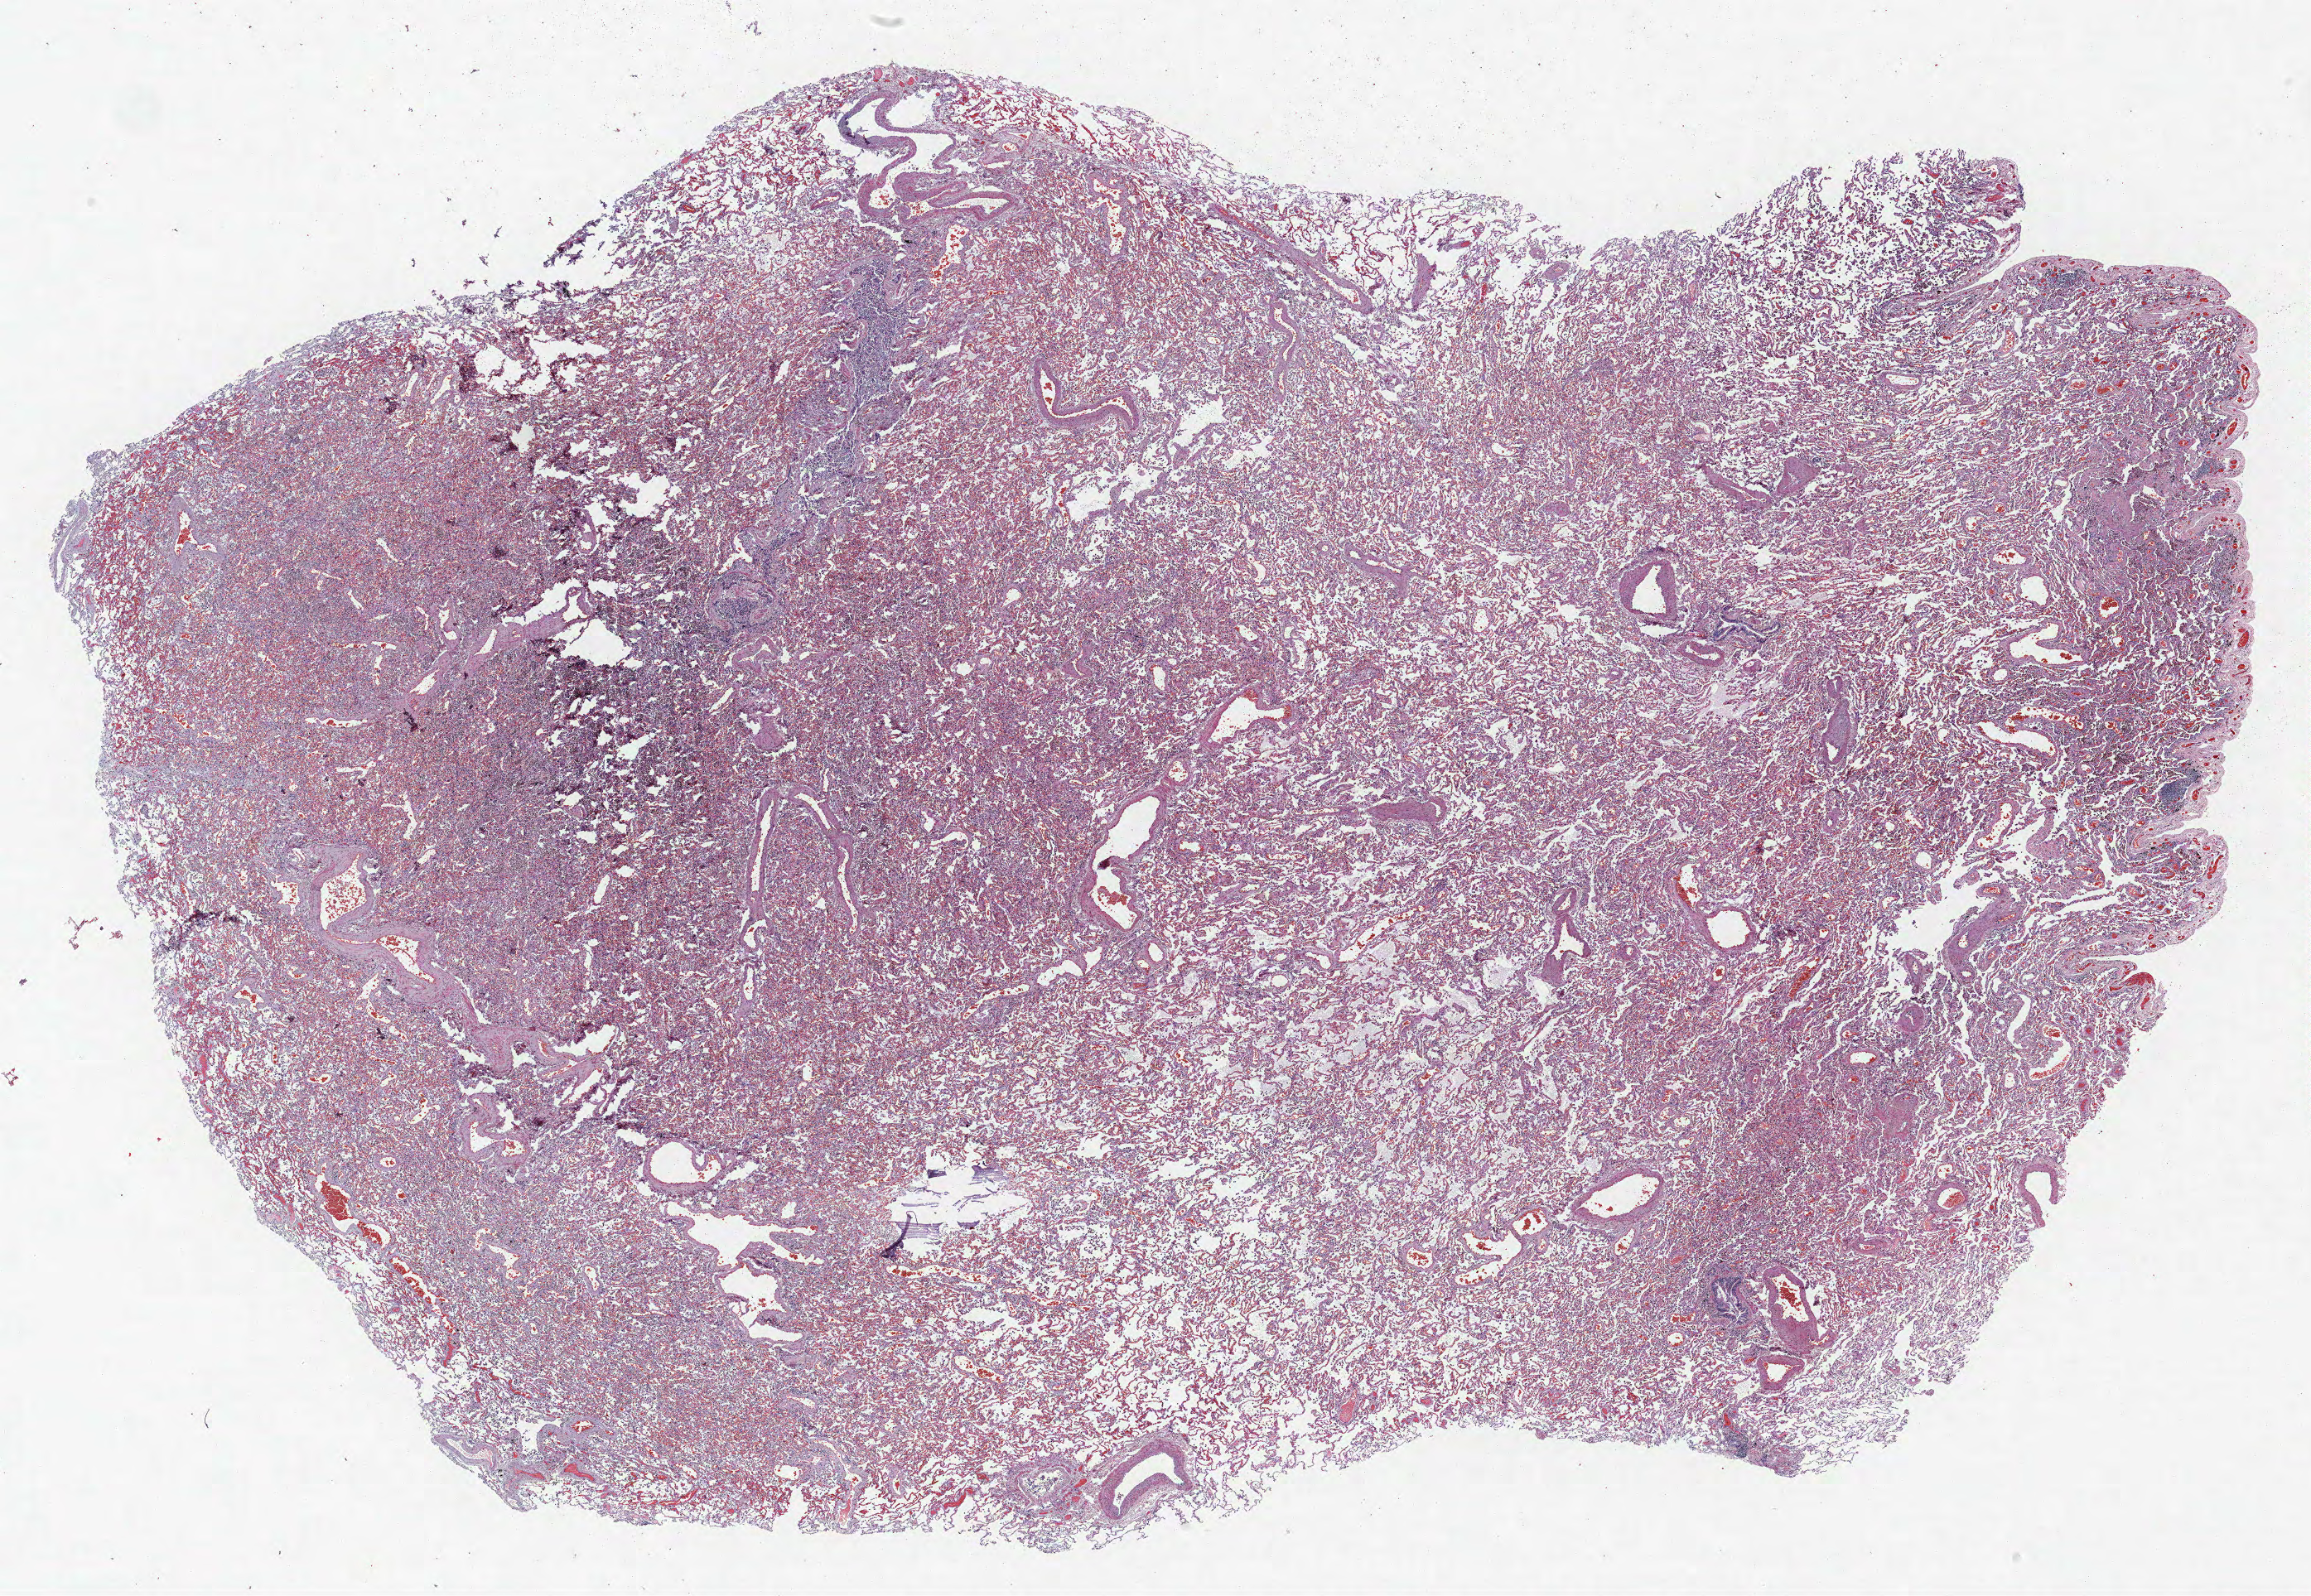
H&E whole-slide image, low-resolution overview of the scanned area, about 22.3 x 15.4 mm (slide scanned at 40x). FFPE section. Lung tissue. Male patient, aged 65 at enrolment. Current smoker at enrolment.
Participant's lung-cancer diagnosis: Carcinoma, NOS.